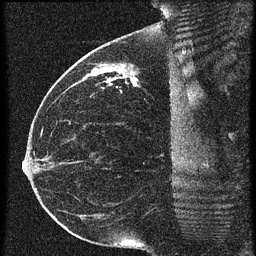
Breast MRI (dynamic contrast-enhanced), one sagittal slice; slice 28 of 60 in the series (ordered by position); 3 images stored at this slice position (order not interpretable as contrast timing); 1.5 T; TE 4.2 ms, TR 20.4 ms; 1.5 mm slice thickness; 256 × 256 image matrix. Female patient, age 35 years. Case-level facts recorded for this patient, not image findings: setting: breast cancer imaged before/during neoadjuvant chemotherapy; receptor status: HR-positive, HER2-negative.
Outlined on this slice (semi-automatic segmentation, software-assisted and operator-edited):
- analysis volume of interest (the breast-tissue region the enhancement analysis was run in; not a lesion): bounding box (x1, y1, x2, y2) in pixels: (84, 50, 179, 97)
- tumour enhancement mask (voxels above the 90 % enhancement threshold inside the analysis volume of interest): (92, 68, 137, 85)